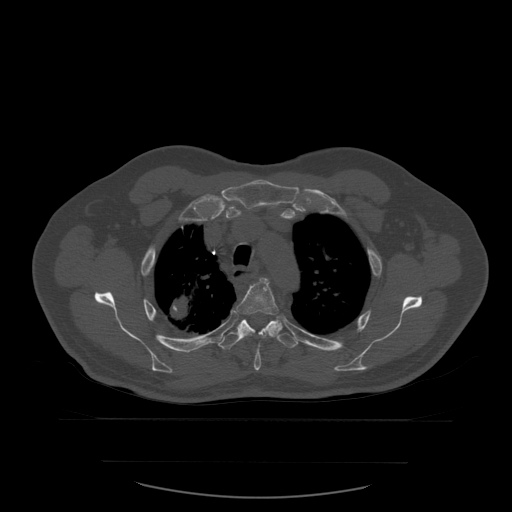
CT including the spine, one axial slice; slice 436 of 590 in the series (ordered by position); bone window (W 1800 / L 400 HU); 1.25 mm slice thickness; 512 × 512 image matrix, field of view 479 × 479 mm. Patient age 71 years. From the clinical record (not read from this slice): primary cancer: lung; vertebrae with lytic lesions (as recorded): T1, T2, L5, S1.
Structures marked on this image (semi-automatic segmentation, software-assisted and operator-edited):
- T4 vertebra: bounding box [x1, y1, x2, y2] px = [236, 278, 283, 371]
- T5 vertebra: [218, 319, 299, 350]